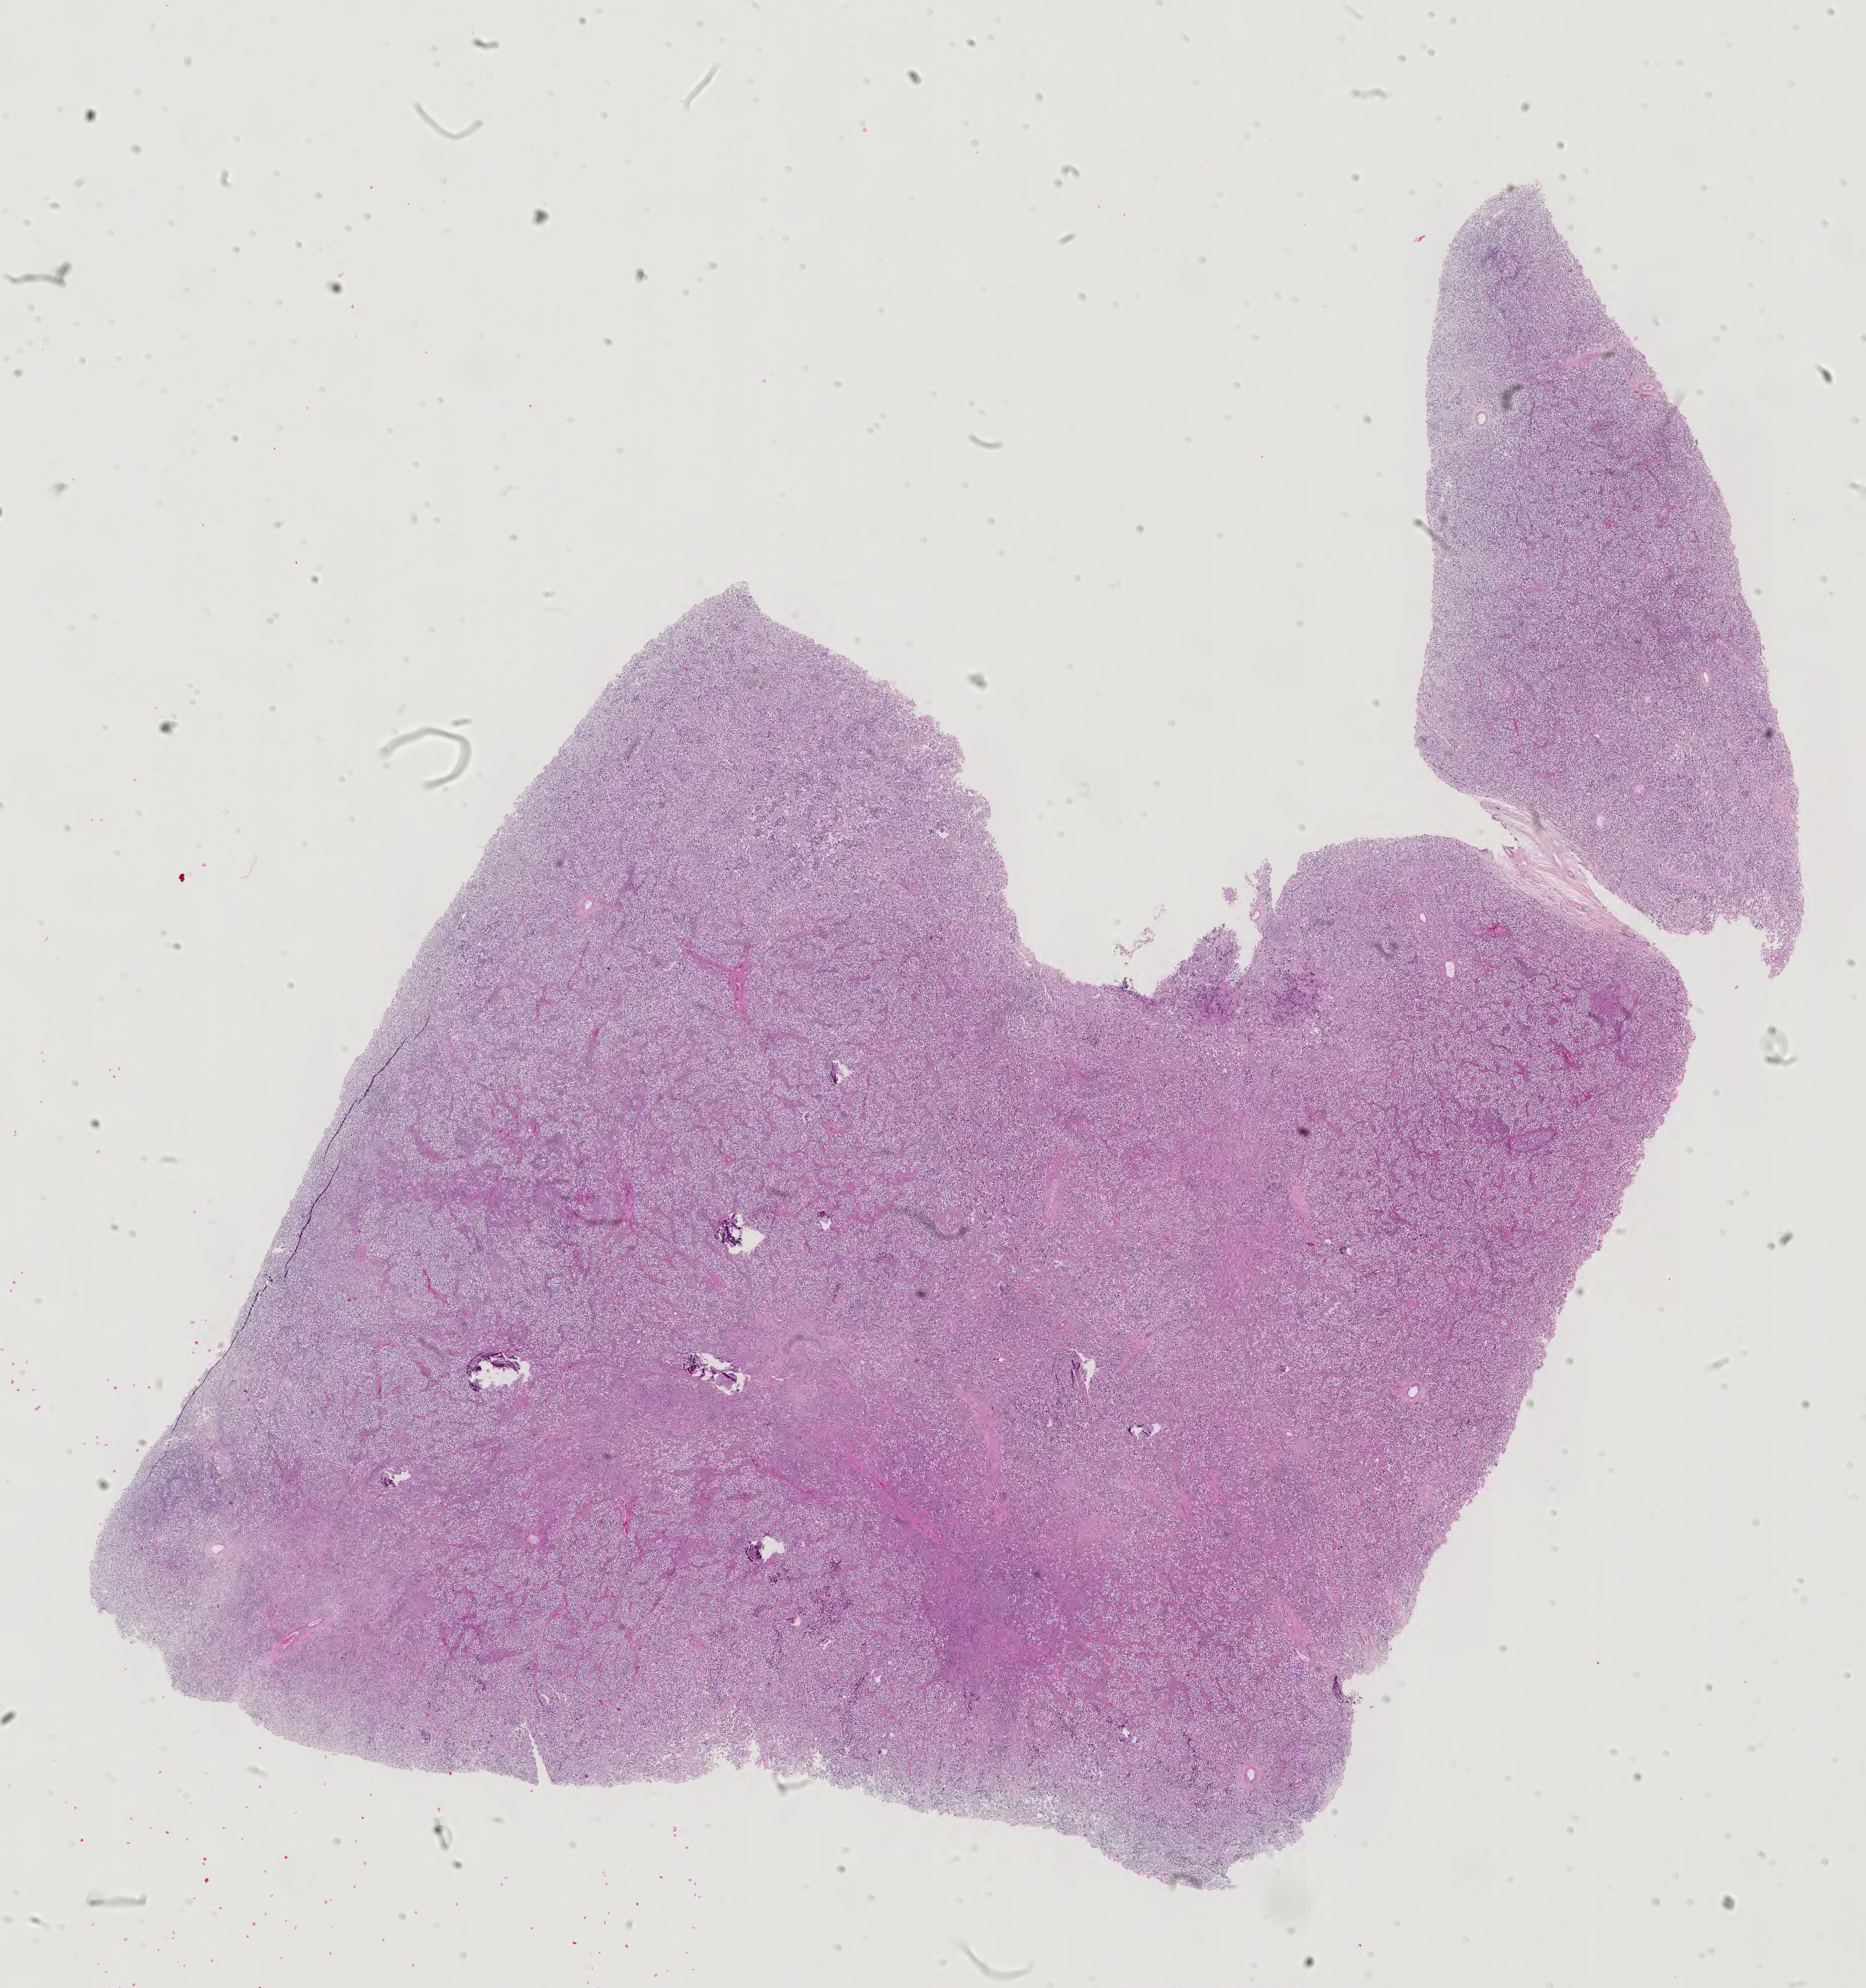
Digitized H&E tissue section (whole slide), whole scanned area (about 18.7 x 19.9 mm, acquisition: 40x scan) shown as a low-resolution overview; FFPE section; testis, primary tumour sample. Patient: male, age at initial diagnosis 28 years.
• AJCC pathologic stage: IS
• diagnosis: Seminoma, NOS
• laterality: right